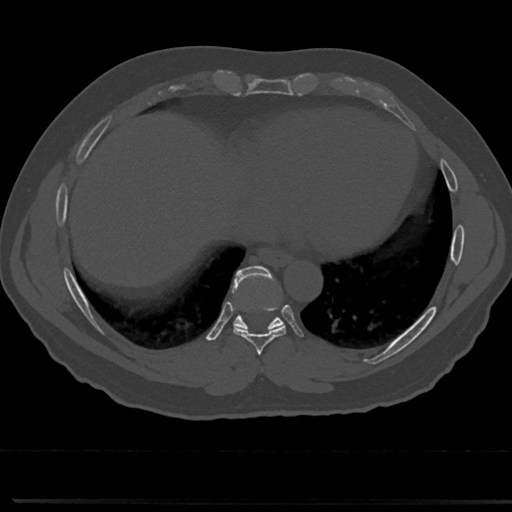
CT including the spine, one axial slice; slice 337 of 817 in the series (ordered by position); reconstruction kernel Br40s/3; bone window (W 1800 / L 400 HU); 0.5 mm slice thickness; 512 × 512 image matrix, field of view 355 × 355 mm. Patient: male, 61 years. Case-level facts recorded for this patient, not image findings: primary cancer: prostate.
Annotated regions visible in this slice (semi-automatic segmentation, software-assisted and operator-edited):
- T7 vertebra: bounding box [x1, y1, x2, y2] px = [258, 345, 266, 377]
- T8 vertebra: [212, 271, 309, 355]